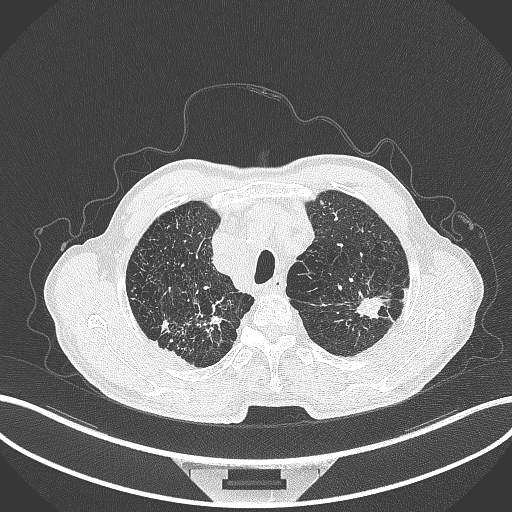
Chest CT, one axial slice. Slice 371 of 463 in the series (ordered by position). 120 kVp. Lung window (W 1500 / L -600 HU). 1 mm slice thickness. 512 × 512 image matrix, field of view 400 × 400 mm. Patient: male, 74 years. From the clinical record (not read from this slice): clinical TNM (as recorded): T2a N1 M0.
Annotated regions visible in this slice (rectangle marked by the reading radiologist):
- lung tumour (recorded histology: adenocarcinoma): bounding box <353,290,389,319> (left, top, right, bottom; pixels)